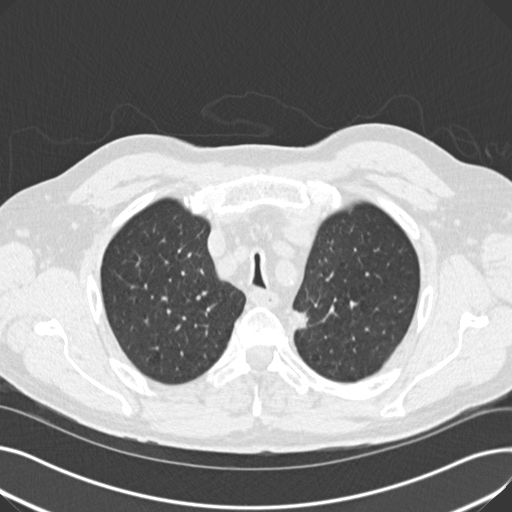
Low-dose screening chest CT, axial slice. Second annual screen. Lung window (W 1500 / L -600 HU). Standard (soft-tissue) reconstruction kernel (B30f). 140 kVp. 512 × 512 image matrix, field of view 370 × 370 mm. Male participant, aged 70 years at enrolment. Current smoker at enrolment.
• Lesion marked by an expert reader, bounding box [x1, y1, x2, y2] px = [280, 298, 320, 340].
• The screening reader recorded 2 non-calcified nodules or masses ≥4 mm on this exam; which of them this box marks is not recorded.
• Official screen result: positive, other.